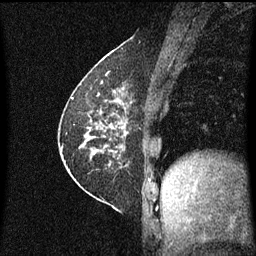
Breast MRI (dynamic contrast-enhanced), one sagittal slice. Slice 24 of 60 in the series (ordered by position). Dynamic contrast-enhanced series, image 2 of 3 at this slice position (ordered by acquisition). 1.5 T. TE 4.2 ms, TR 8.4 ms. 256 × 256 image matrix, field of view 200 × 200 mm. Patient: female, 60 years.
Outlined on this slice (semi-automatic segmentation, software-assisted and operator-edited):
- analysis volume of interest (the breast-tissue region the enhancement analysis was run in; not a lesion): bounding box <69,66,132,193> (left, top, right, bottom; pixels)
- tumour enhancement mask (voxels above the 70 % enhancement threshold inside the analysis volume of interest): <87,90,128,153>